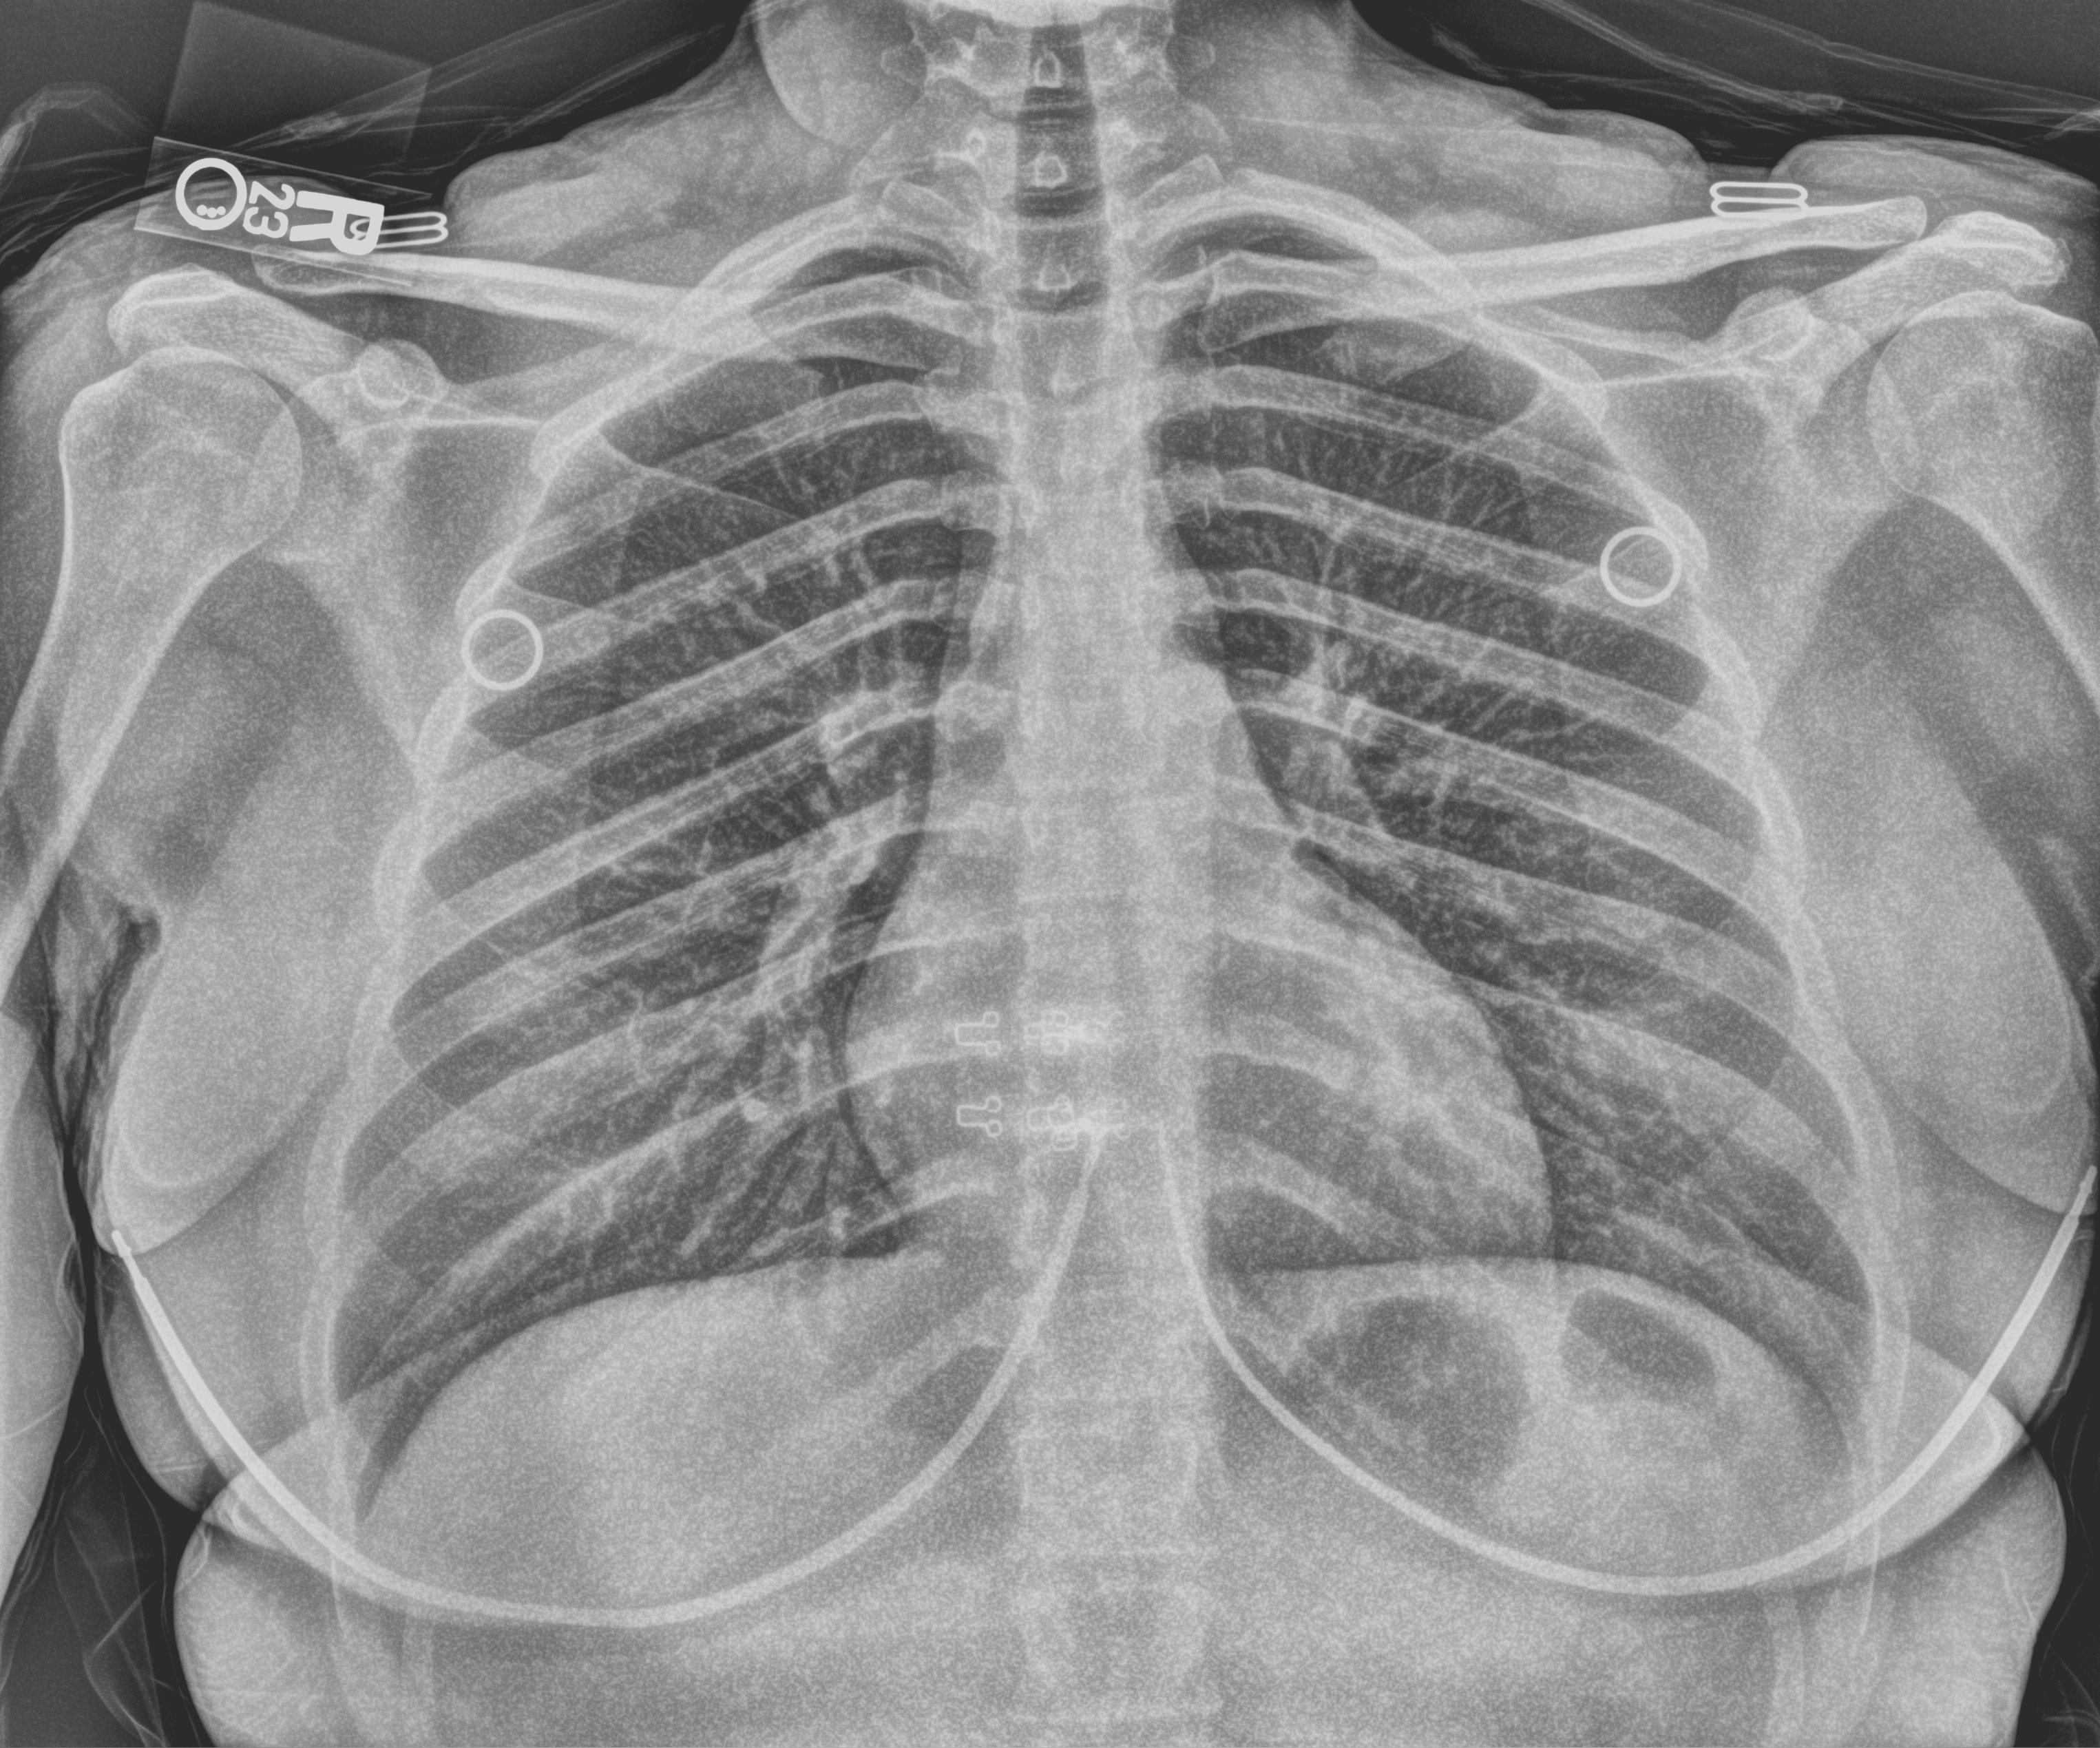
Chest X-ray (portable); anteroposterior (AP) projection. Patient hospitalised with COVID-19; female, aged 18–59 years.
From the hospital-stay record, not from the radiograph (when in the stay this image was taken is not recorded):
- admitted to intensive care during this hospital stay: no
- mechanically ventilated during this hospital stay: no